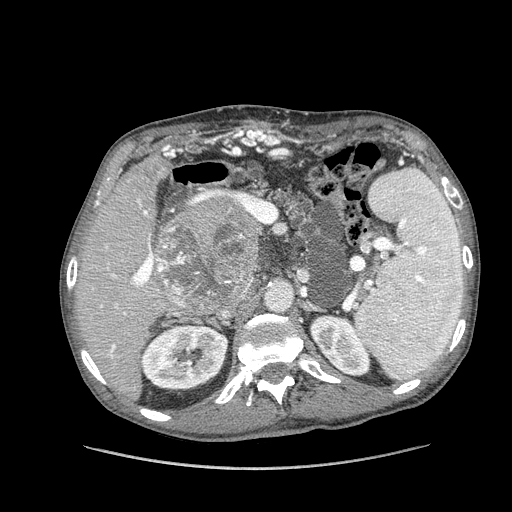
Contrast-enhanced abdominal CT (liver protocol), one axial slice. Slice 75 of 162 in the series (ordered by position). Reconstruction kernel STANDARD. Soft-tissue window (W 400 / L 40 HU). 2.5 mm slice thickness. 512 × 512 image matrix, field of view 400 × 400 mm. From the clinical record (not read from this slice): diagnosis: hepatocellular carcinoma (patient treated with transarterial chemoembolisation; whether this scan precedes or follows treatment is not stated here); TNM stage (as recorded): Stage-IIIA; Child-Pugh class: A; tumour nodularity: multinodular.
Structures marked on this image (semi-automatically segmented with operator editing):
- liver parenchyma outside the tumour (the mass and vessels are separate outlines, so this box may not span the whole liver): bounding box (x1, y1, x2, y2) in pixels: (76, 154, 262, 399)
- mass: (152, 198, 259, 313)
- liver vessels: (100, 199, 152, 358)